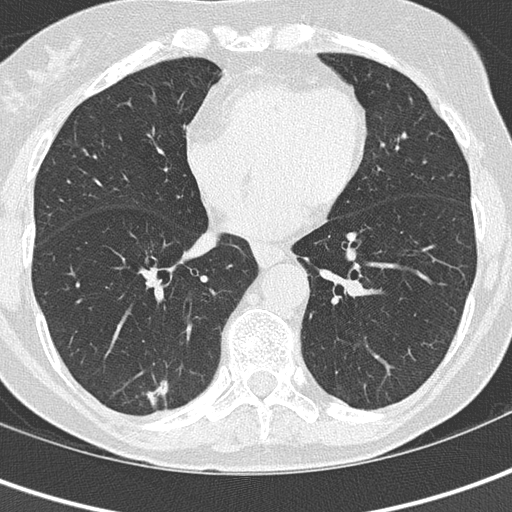
Axial slice from a low-dose chest CT screening exam, second screening round (one year after baseline), lung window (W 1500 / L -600 HU), 2 mm slice thickness, lung (sharp) reconstruction kernel (B50f), 120 kVp, 512 × 512 image matrix. Female participant, aged 69 years at enrolment. Current smoker at enrolment.
- Expert-annotated lung lesion, bounding box <123,363,184,421> (left, top, right, bottom; pixels).
- The screening reader recorded 2 non-calcified nodules or masses ≥4 mm on this exam; which of them this box marks is not recorded.
- Later outcome: lung cancer diagnosed 112 days after this screen — adenocarcinoma, NOS, right lower lobe, moderately differentiated (G2), stage IA (AJCC 6th edition), 16 mm at pathology.